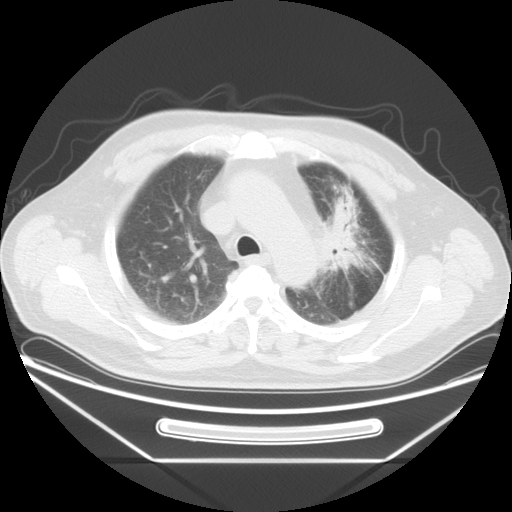
Chest CT, one axial slice; position 29 of 38 along the scan axis; 120 kVp; lung window (W 1500 / L -600 HU); 5 mm slice thickness; 512 × 512 image matrix, field of view 411 × 411 mm. Male patient, age 61 years. Case-level facts recorded for this patient, not image findings: clinical TNM (as recorded): T2a N0 M0; histopathological grade: G3.
Outlined on this slice (rectangle marked by the reading radiologist):
- lung tumour (recorded histology: small cell carcinoma): bounding box [x1, y1, x2, y2] px = [320, 193, 372, 280]